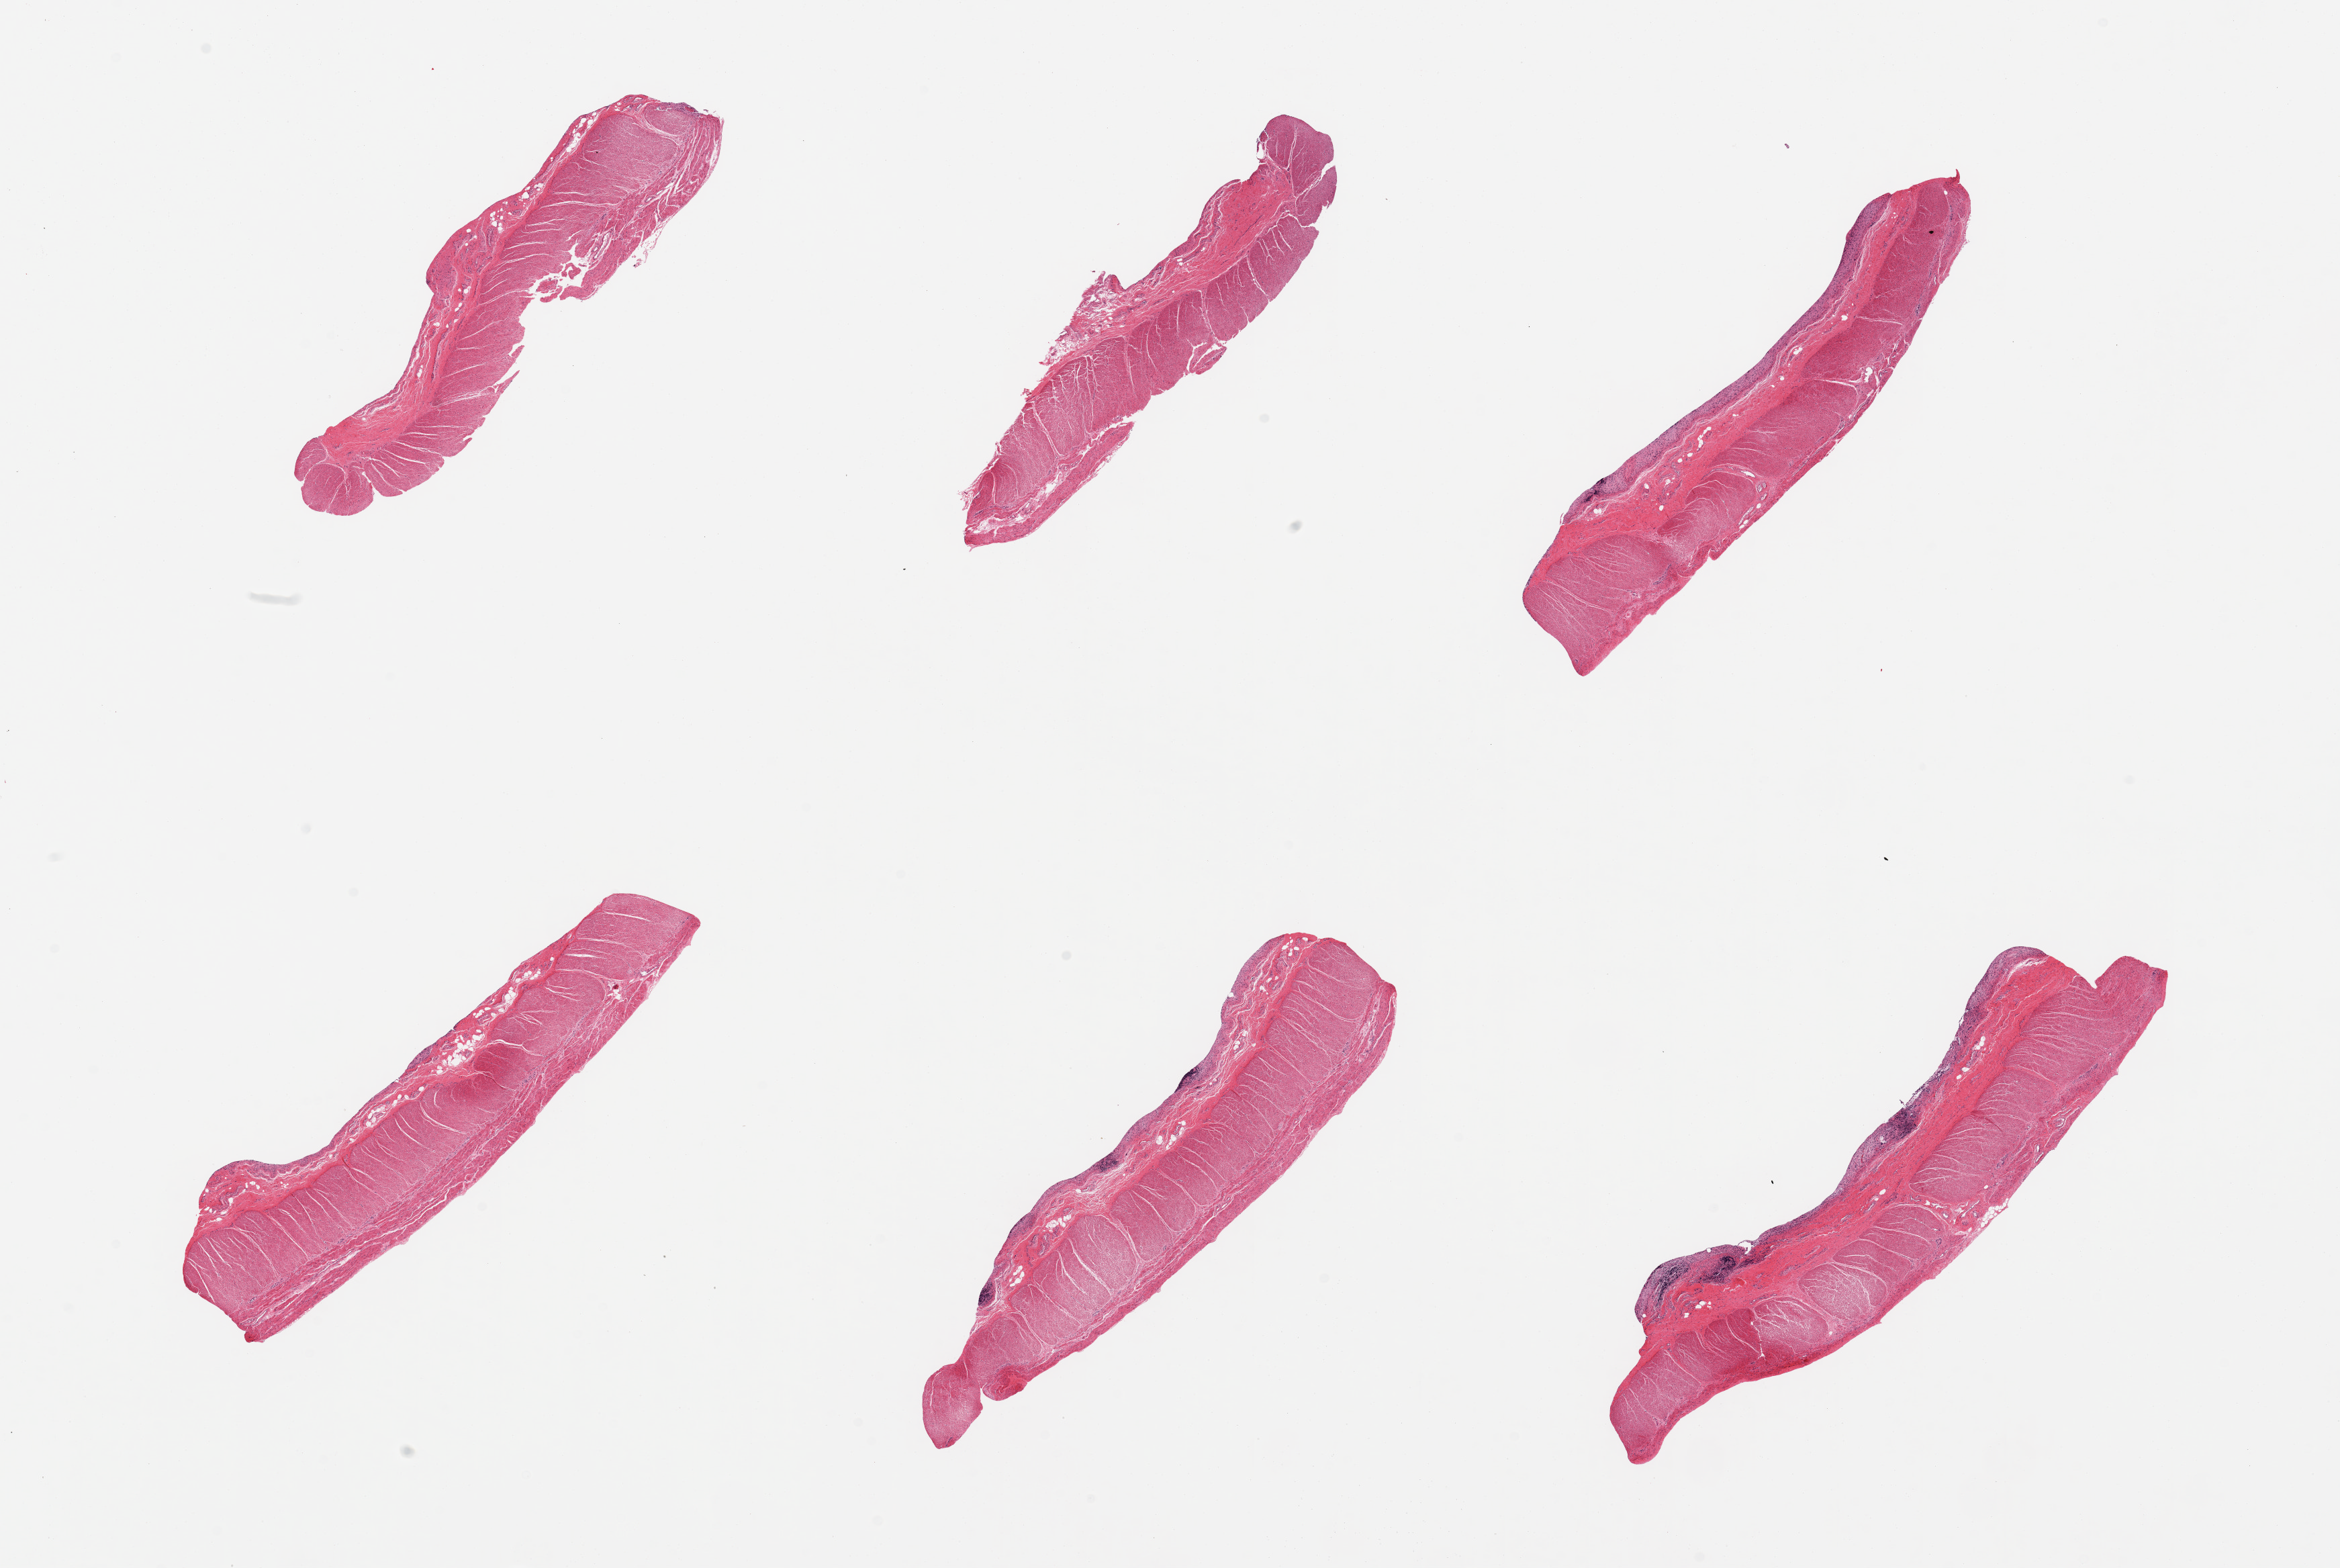
Digitized H&E-stained section, shown as a low-resolution overview of the whole scanned area (about 27.6 x 18.5 mm, slide scanned at 20x); PAXgene-fixed paraffin-embedded (PFPE) section; section of sigmoid colon (target tissue); tissue donor sample. Donor: female.
Pathologist's review note for this sample: 6 pieces, all muscularis.